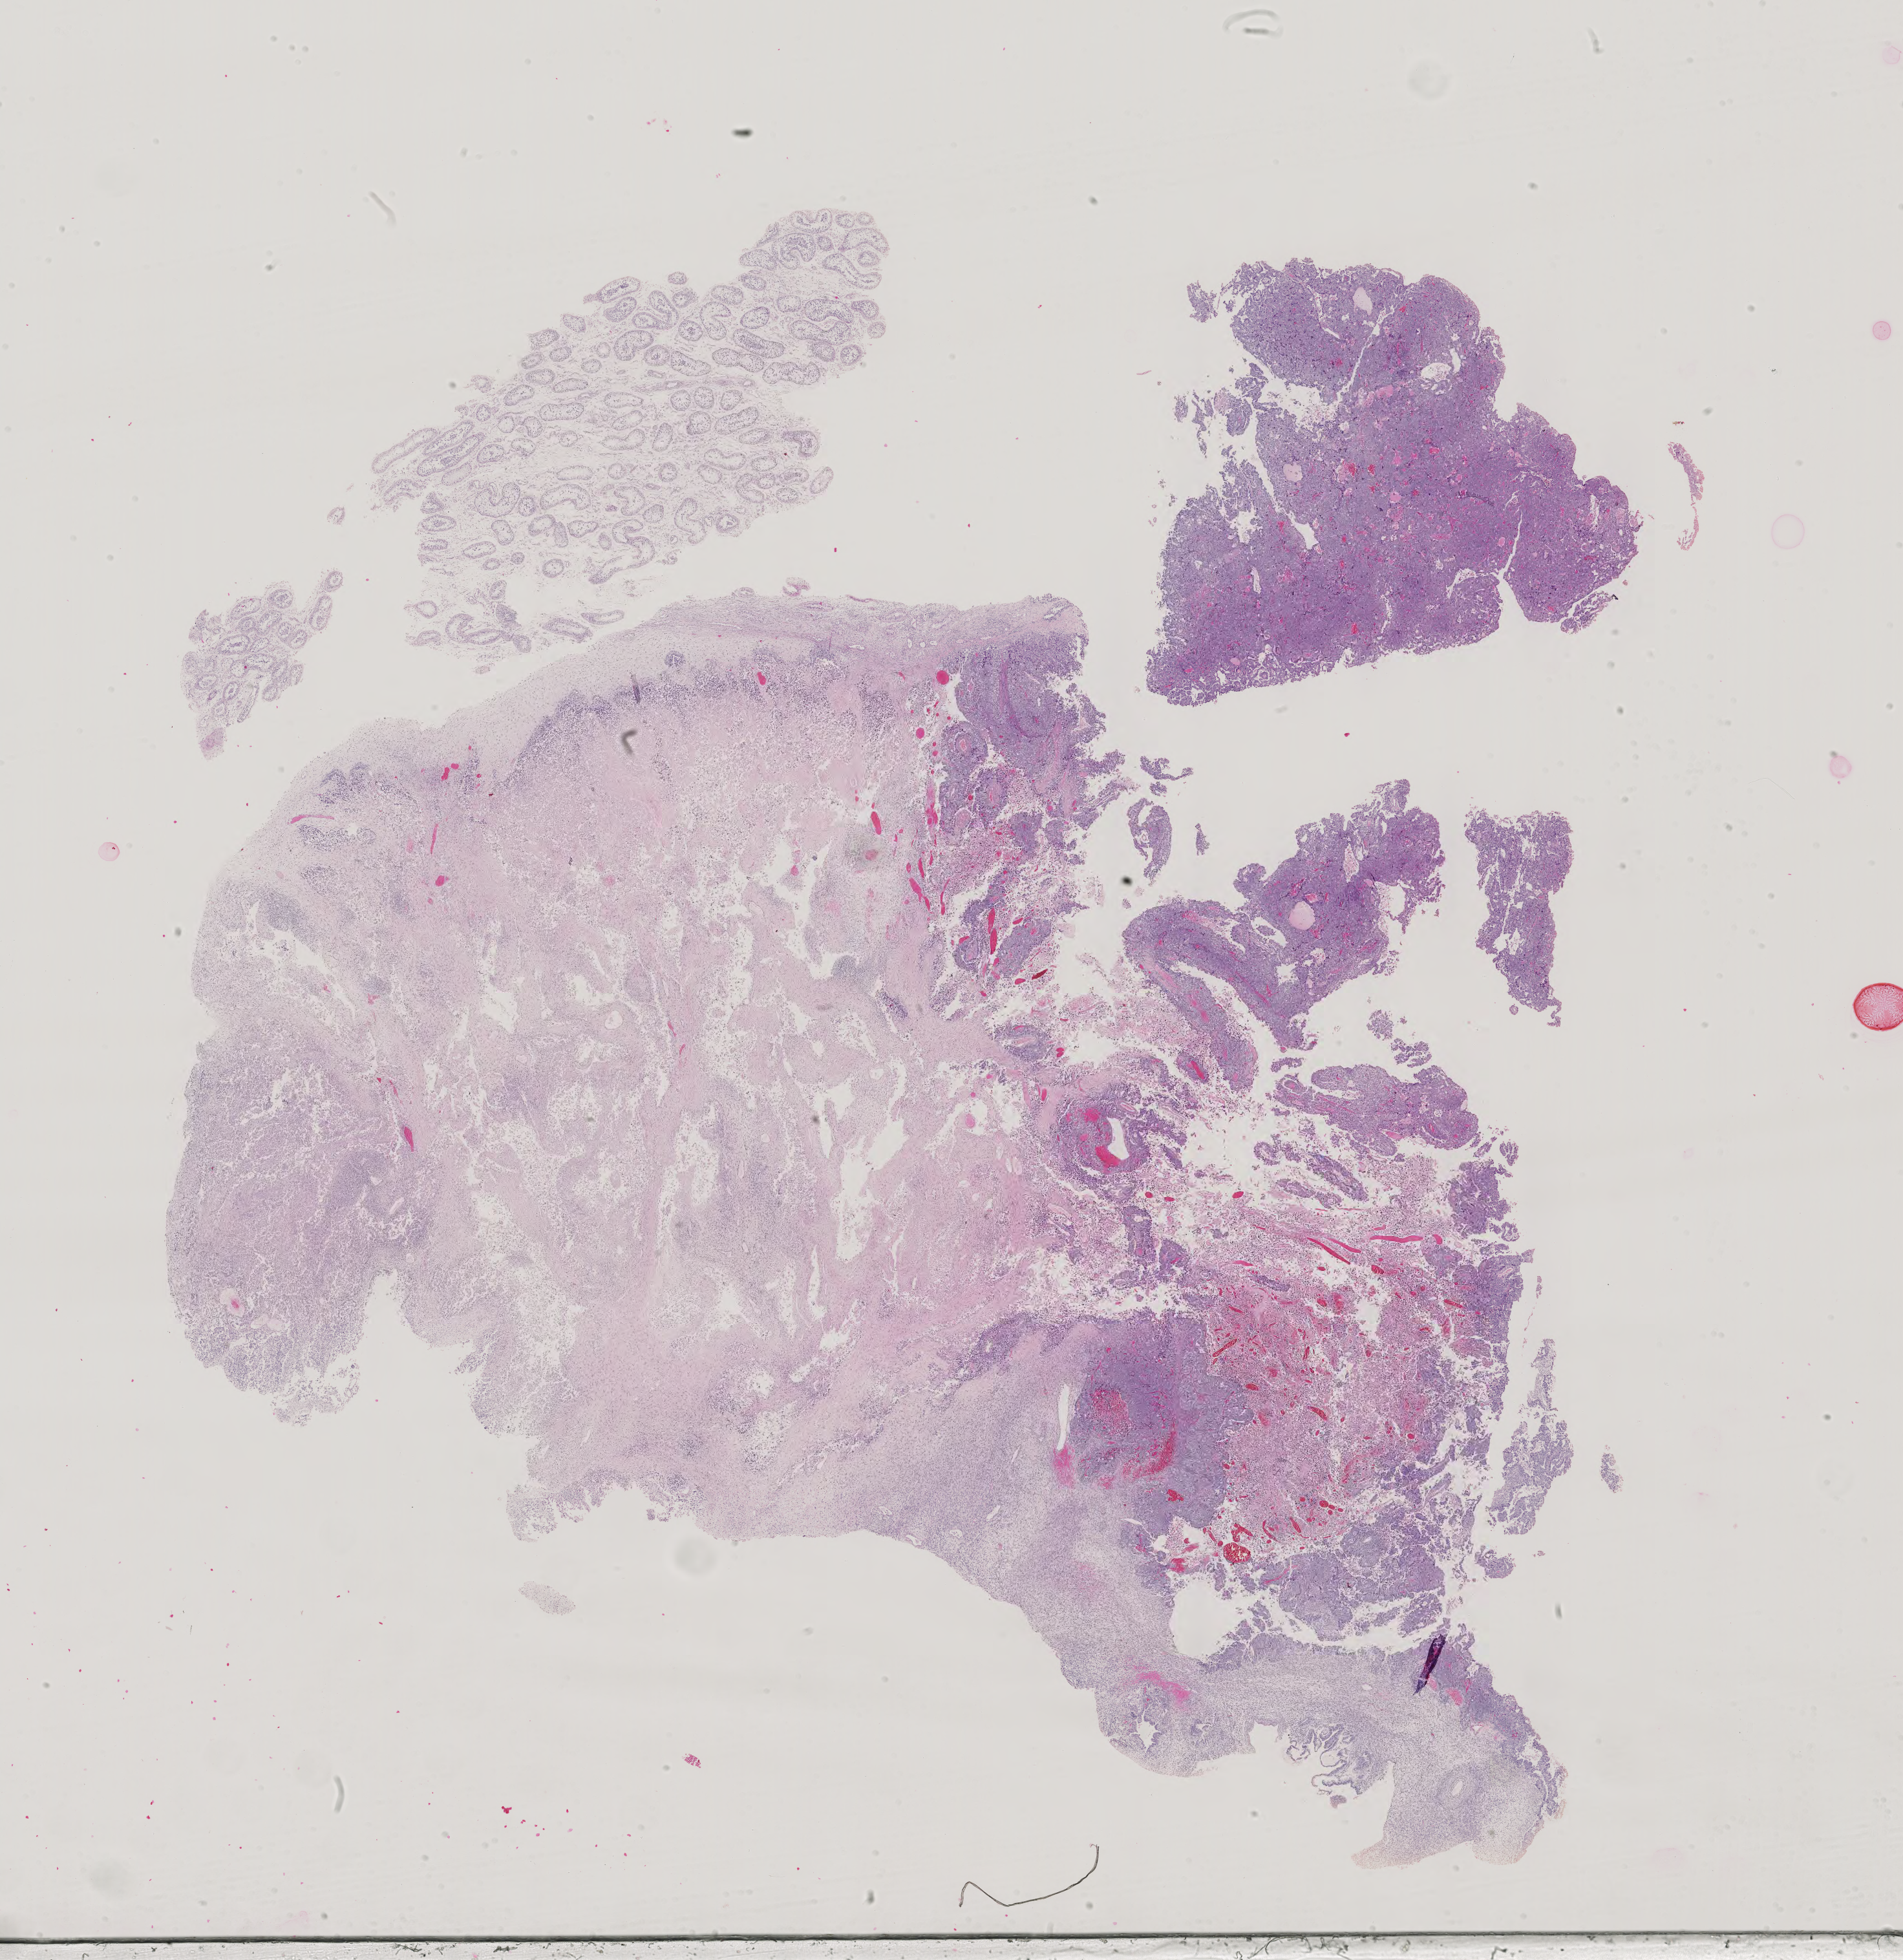
Hematoxylin and eosin (H&E) stained whole-slide image, a low-resolution overview of the entire scanned area, about 21.5 x 22.1 mm (from a 40x scan). Male patient.
Specimen: formalin-fixed paraffin-embedded (FFPE) diagnostic section; sample: primary tumour, testis.